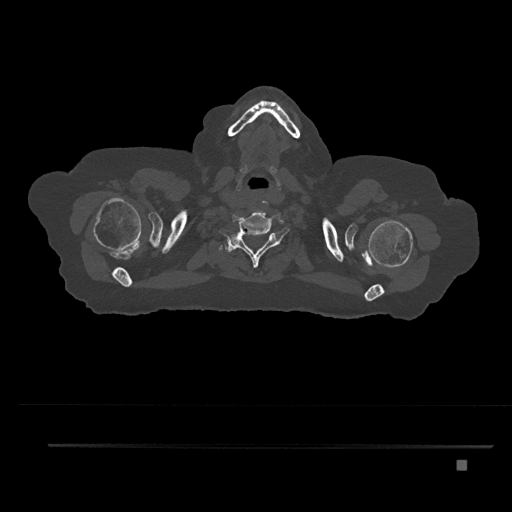
CT including the spine, one axial slice. Slice 725 of 797 in the series (ordered by position). Bone window (W 1800 / L 400 HU). 0.5 mm slice thickness. 512 × 512 image matrix, field of view 437 × 437 mm. Female patient, age 76 years. From the clinical record (not read from this slice): primary cancer: lung.
Annotated regions visible in this slice (semi-automatically segmented with operator editing):
- T1 vertebra: bounding box [x1, y1, x2, y2] px = [226, 240, 261, 255]